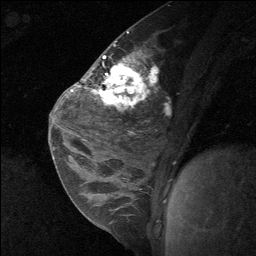
Breast MRI (dynamic contrast-enhanced), one sagittal slice; slice 36 of 64 in the series (ordered by position); dynamic contrast-enhanced study with each time point stored as its own series, time point 2 of 3 at this slice position (early post-contrast, ordered by acquisition time); 1.5 T; TE 4.8 ms, TR 27 ms; 2 mm slice thickness; 256 × 256 image matrix, field of view 180 × 180 mm. Patient: female, 26 years. Case-level facts recorded for this patient, not image findings: setting: breast cancer imaged before/during neoadjuvant chemotherapy; receptor status: HR-positive, HER2-negative.
Outlined on this slice (semi-automatic segmentation, software-assisted and operator-edited):
- analysis volume of interest (the breast-tissue region the enhancement analysis was run in; not a lesion): bounding box [x1, y1, x2, y2] px = [86, 43, 152, 138]
- tumour enhancement mask (voxels above the 90 % enhancement threshold inside the analysis volume of interest): [92, 62, 137, 105]